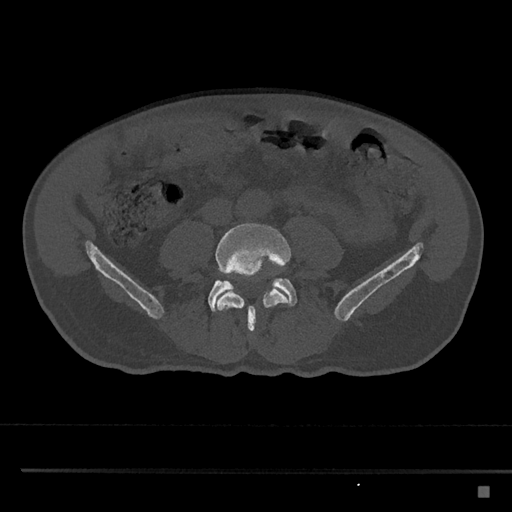
CT including the spine, one axial slice; position 613 of 797 along the scan axis; reconstruction kernel Br40s/3; bone window (W 1800 / L 400 HU); 512 × 512 image matrix, field of view 391 × 391 mm. Male patient, age 59 years. Case-level facts recorded for this patient, not image findings: primary cancer: prostate.
Structures marked on this image (semi-automatic segmentation, software-assisted and operator-edited):
- L4 vertebra: bounding box (x1, y1, x2, y2) in pixels: (215, 223, 291, 332)
- L5 vertebra: (208, 275, 298, 312)